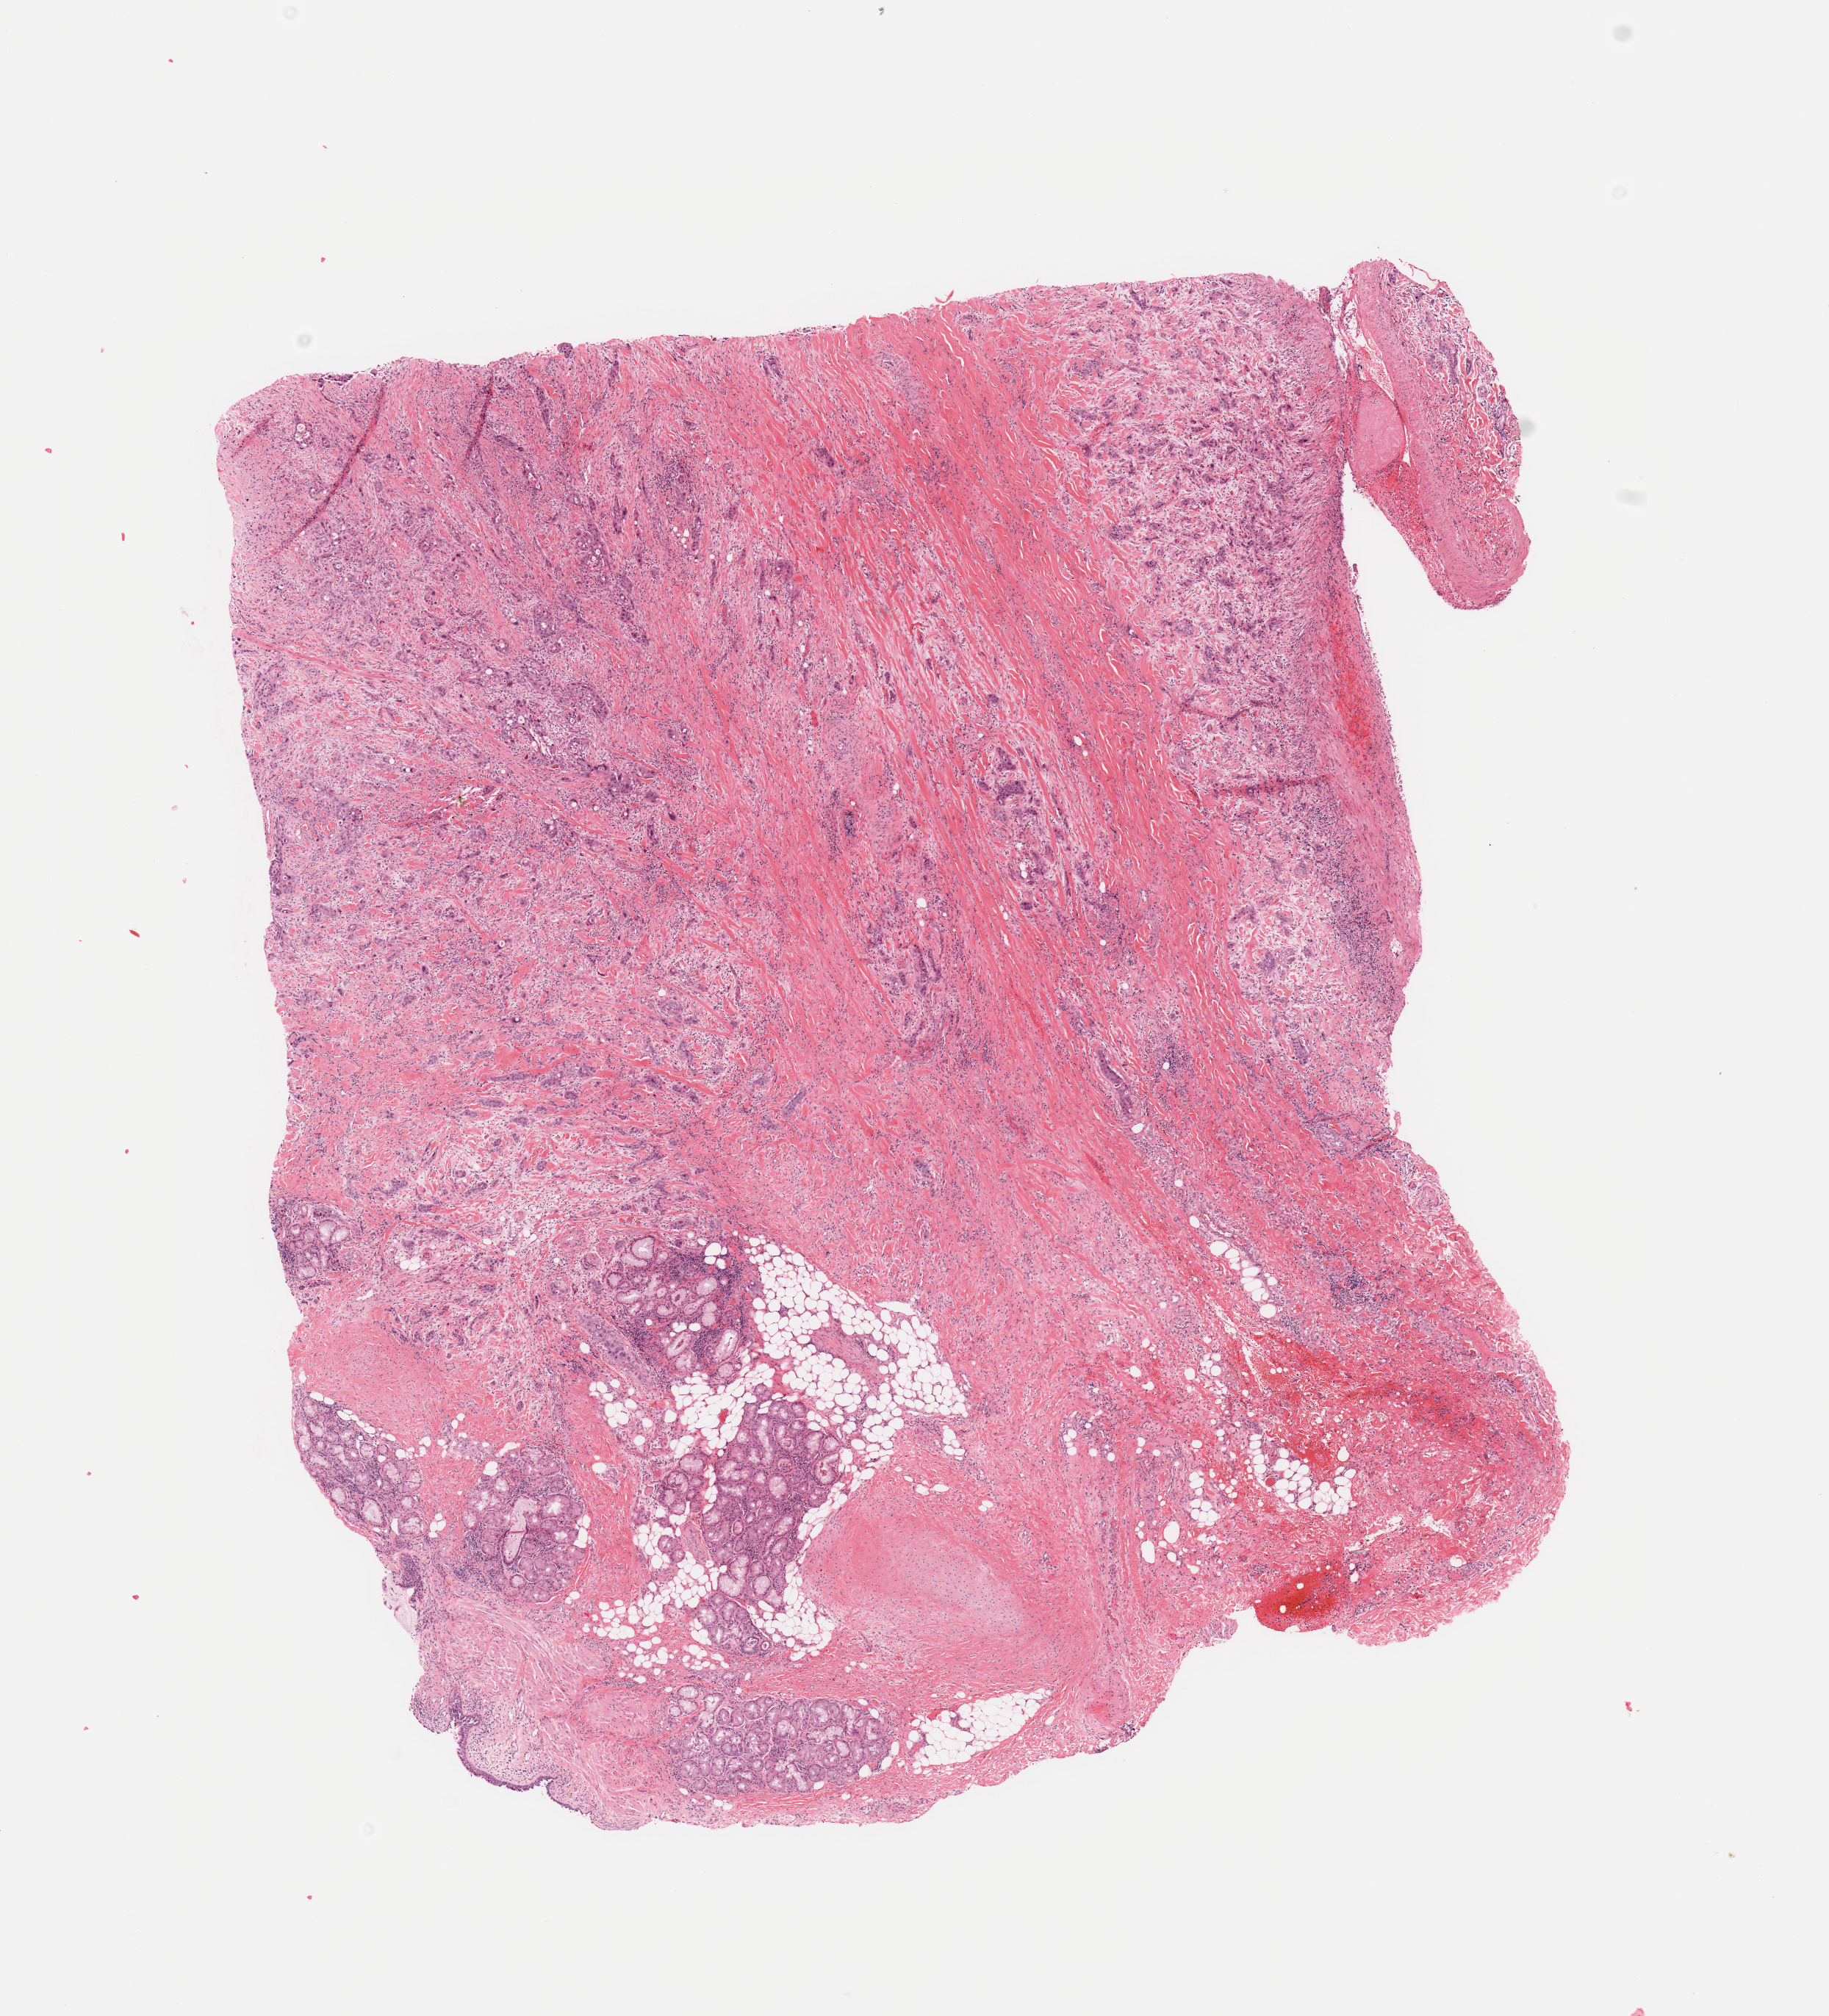
Hematoxylin and eosin (H&E) stained whole-slide image, low-resolution overview of the scanned area, about 9.8 x 10.9 mm; lung, tumour tissue. Patient: male, age 40 years. Histologic grade: G3 (poorly differentiated).
• AJCC pathologic stage: IIIA
• diagnosis: Squamous cell carcinoma, NOS
• primary tumour site (as recorded): right middle lobe